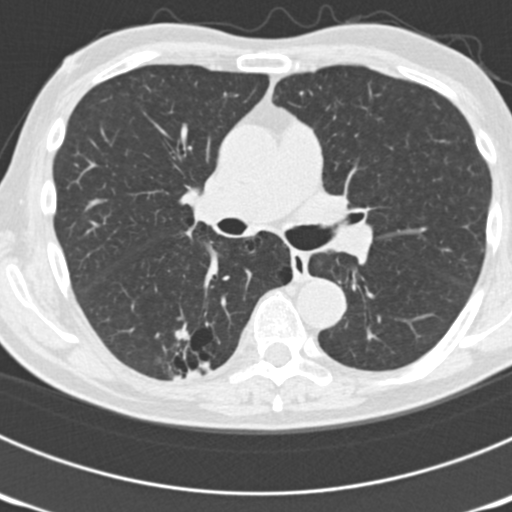
Chest CT (low-dose screening protocol), one axial image, third screening round (two years after baseline), lung window (W 1500 / L -600 HU), 2 mm slice thickness, 120 kVp, 512 × 512 image matrix. Male participant, aged 70 years at enrolment.
Lesion marked by an expert reader, bounding box [x1, y1, x2, y2] px = [144, 309, 237, 385]. The screening reader recorded 3 non-calcified nodules or masses ≥4 mm on this exam; which of them this box marks is not recorded. Official screen result: positive, other. Later outcome: lung cancer diagnosed 14 days after this screen — bronchiolo-alveolar adenocarcinoma, NOS, right lower lobe, poorly differentiated (G3), stage IB (AJCC 6th edition), 30 mm at pathology.